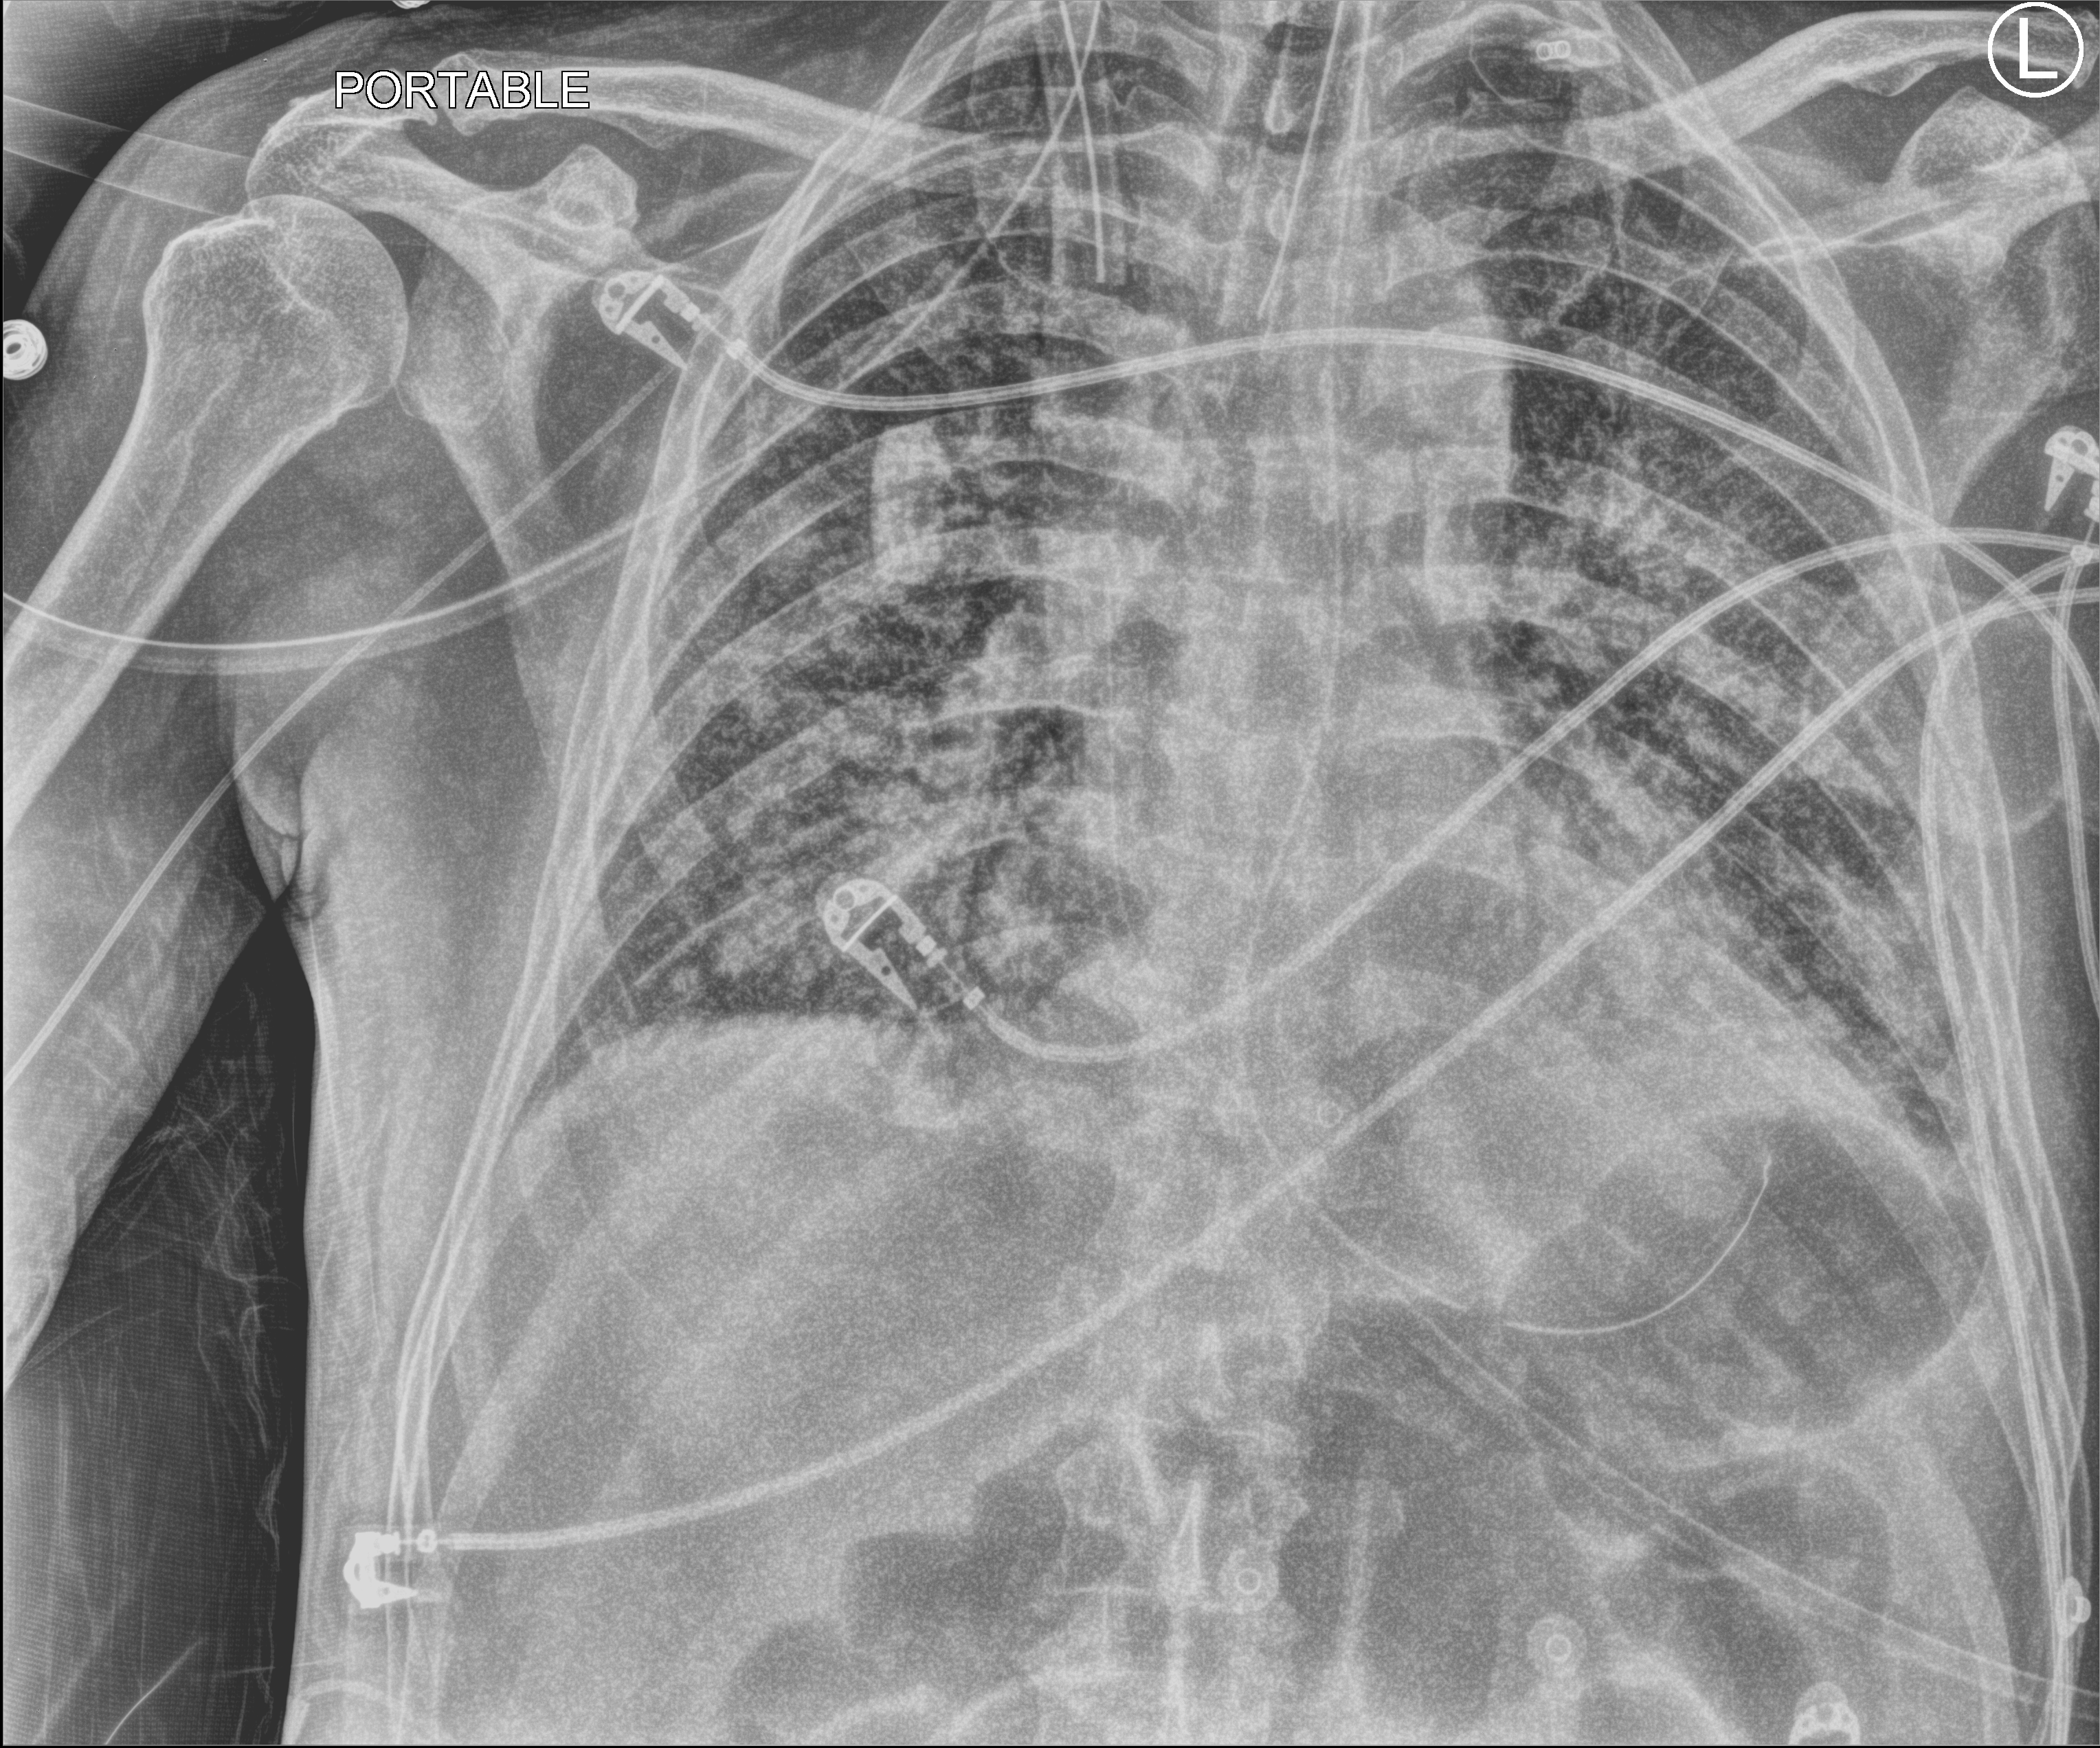
Chest X-ray (portable); anteroposterior (AP) projection. Patient hospitalised with COVID-19; male, aged 60–74 years.
Hospital-stay facts (about this admission, not read from this image; timing relative to this image not recorded): admitted to intensive care during this hospital stay: yes.